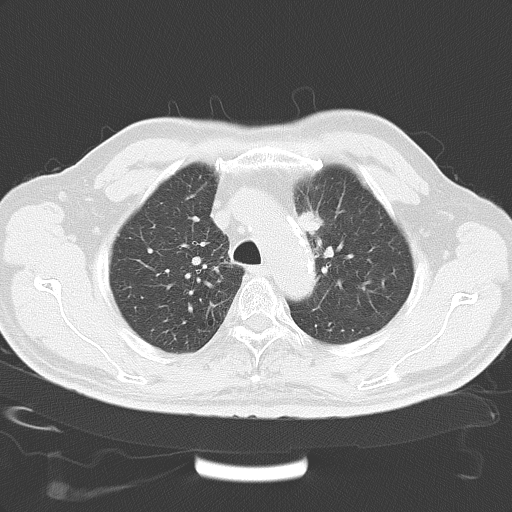
Chest CT, one axial slice. Slice 40 of 51 in the series (ordered by position). Reconstruction kernel B70f. Lung window (W 1500 / L -600 HU). 5 mm slice thickness. 512 × 512 image matrix. Male patient, age 67 years. From the clinical record (not read from this slice): clinical TNM (as recorded): T1a N2 M1a.
Annotated regions visible in this slice (rectangle marked by the reading radiologist):
- lung tumour (recorded histology: large cell carcinoma): bounding box <298,204,328,242> (left, top, right, bottom; pixels)